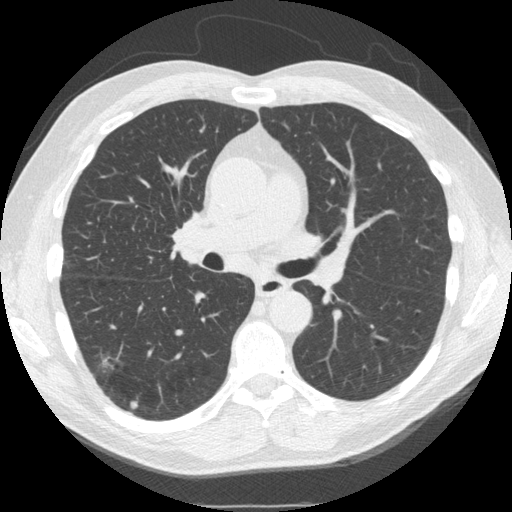
Low-dose screening chest CT, one axial slice. Position 94 of 162 along the scan axis. Lung window (W 1500 / L -600 HU). 2.5 mm slice thickness. 512 × 512 image matrix, field of view 360 × 360 mm.
Structures marked on this image (outlined manually by an expert reader):
- lesion 1 (nodule, lower lobe of right lung): bounding box (x1, y1, x2, y2) in pixels: (102, 357, 113, 369)
- lesion 2 (tumor, lower lobe of right lung): (130, 400, 138, 409)